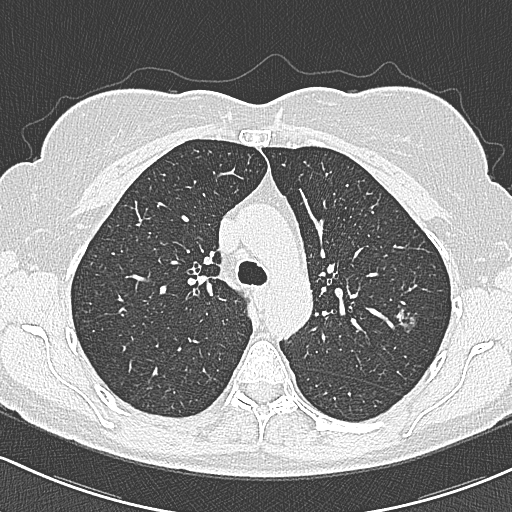
Chest CT (low-dose screening protocol), one axial image; baseline screening round; lung window (W 1500 / L -600 HU); 1 mm slice thickness; 120 kVp; slice 92 of 312 in the series. Female participant, aged 65 years at enrolment. Current smoker at enrolment.
Expert reader's lesion annotation, box from (x=387, y=300) to (x=426, y=337) px. The screening reader recorded 3 non-calcified nodules or masses ≥4 mm on this exam; which of them this box marks is not recorded. Official screen result: positive, change unspecified: nodule(s) >= 4 mm or enlarging nodule(s), mass(es), or other non-specific abnormalities suspicious for lung cancer.